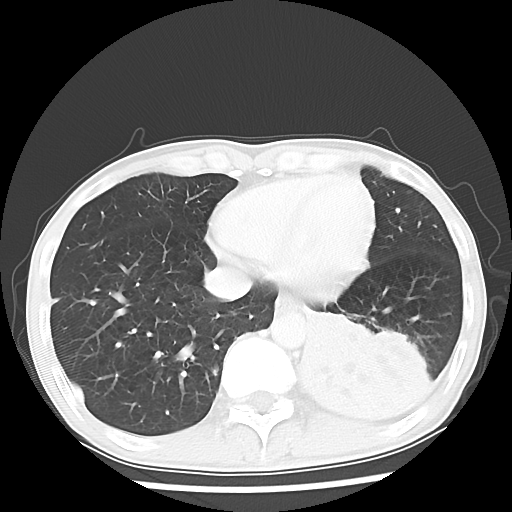
Chest CT, one axial slice. Slice 16 of 64 in the series (ordered by position). Reconstruction kernel LUNG. Lung window (W 1500 / L -600 HU). 5 mm slice thickness. 512 × 512 image matrix, field of view 313 × 313 mm. Patient: male, 68 years. Case-level facts recorded for this patient, not image findings: clinical TNM (as recorded): T4 N0 M0.
Structures marked on this image (bounding box drawn by a radiologist):
- lung tumour (recorded histology: squamous cell carcinoma): bounding box (x1, y1, x2, y2) in pixels: (289, 304, 448, 456)